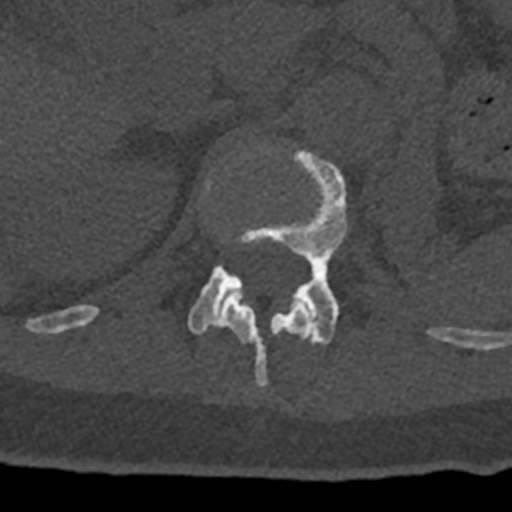
CT including the spine, one axial slice. Position 461 of 797 along the scan axis. Reconstruction kernel Br40s/3. 120 kVp. Bone window (W 1800 / L 400 HU). 512 × 512 image matrix, field of view 160 × 160 mm. Patient: male, 74 years. Case-level facts recorded for this patient, not image findings: primary cancer: renal; vertebrae with lytic lesions (as recorded): T10, L1, L2, L3, L4, L5.
Annotated regions visible in this slice (semi-automatic segmentation, software-assisted and operator-edited):
- L1 vertebra: bounding box (x1, y1, x2, y2) in pixels: (188, 147, 348, 344)
- T12 vertebra: (70, 181, 432, 387)